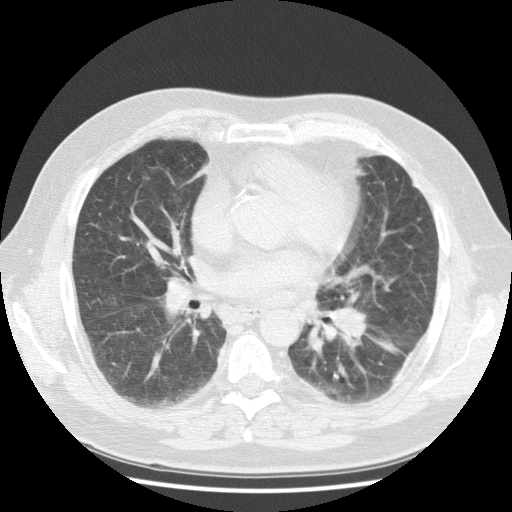
Low-dose screening chest CT, one axial slice; reconstruction kernel STANDARD; 120 kVp; lung window (W 1500 / L -600 HU); 2.5 mm slice thickness; 512 × 512 image matrix, field of view 350 × 350 mm.
Outlined on this slice (expert manual segmentation):
- lesion 1 (tumor, hilum of left lung): bounding box (x1, y1, x2, y2) in pixels: (333, 306, 368, 339)